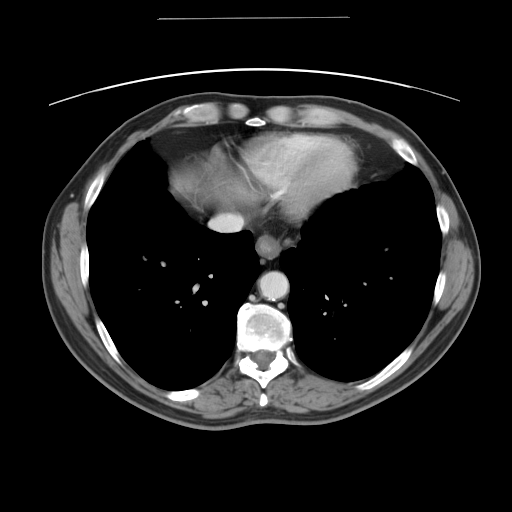
Contrast-enhanced abdominal CT, one axial slice; slice 46 of 49 in the series (ordered by position); 120 kVp; soft-tissue window (W 400 / L 40 HU); 512 × 512 image matrix, field of view 413 × 413 mm. Male patient, age 57 years. Case-level facts recorded for this patient, not image findings: diagnosis: colorectal cancer liver metastases, imaged before liver resection; multiple liver metastases: yes; largest metastasis: 4 cm.
Outlined on this slice (manually delineated by an expert):
- liver: bounding box (x1, y1, x2, y2) in pixels: (166, 154, 258, 209)
- planned liver remnant (the part of the liver to remain after resection): (208, 154, 258, 208)